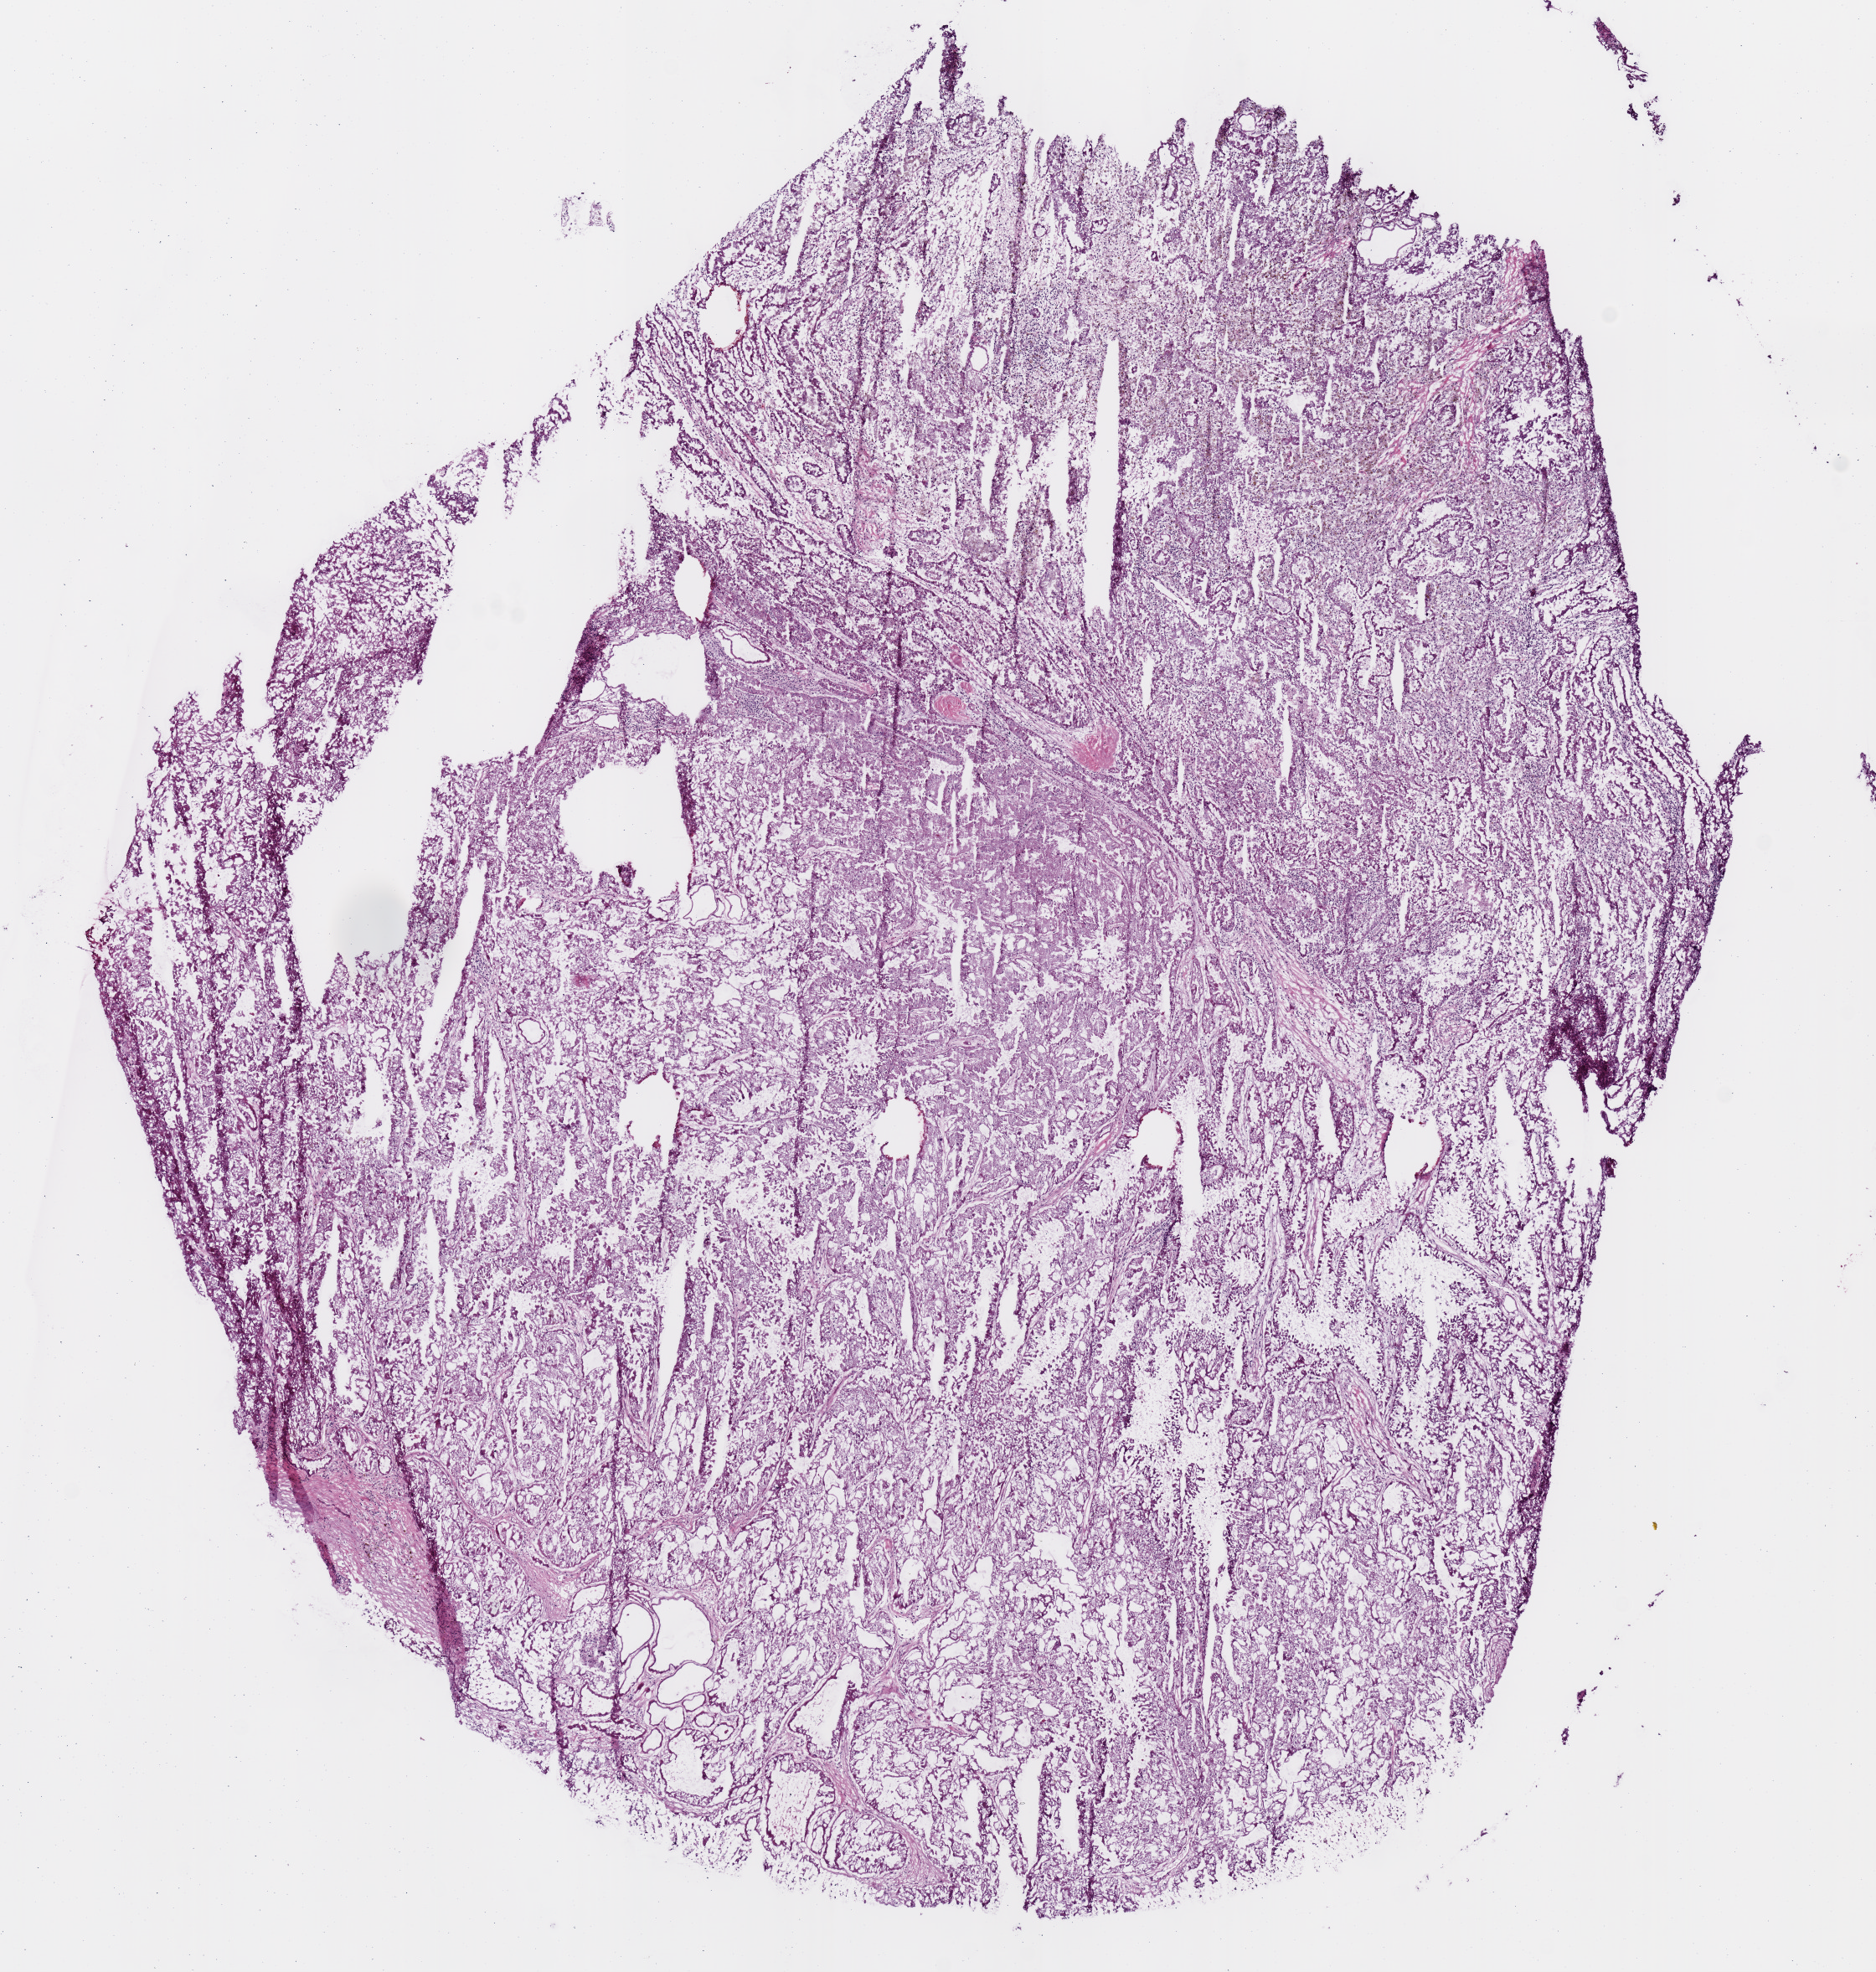
Hematoxylin and eosin (H&E) stained whole-slide image, low-resolution overview of the scanned area, about 8.9 x 9.3 mm (acquisition: 20x scan). Frozen section from the top of the tissue portion. Sample: primary tumour, kidney. Patient: male, age at initial diagnosis 48 years. Composition of this section per pathologist review: tumour nuclei 80%, necrosis 0%.
* pathologic diagnosis: Papillary adenocarcinoma, NOS
* AJCC pathologic stage: I (7th edition)
* laterality: left